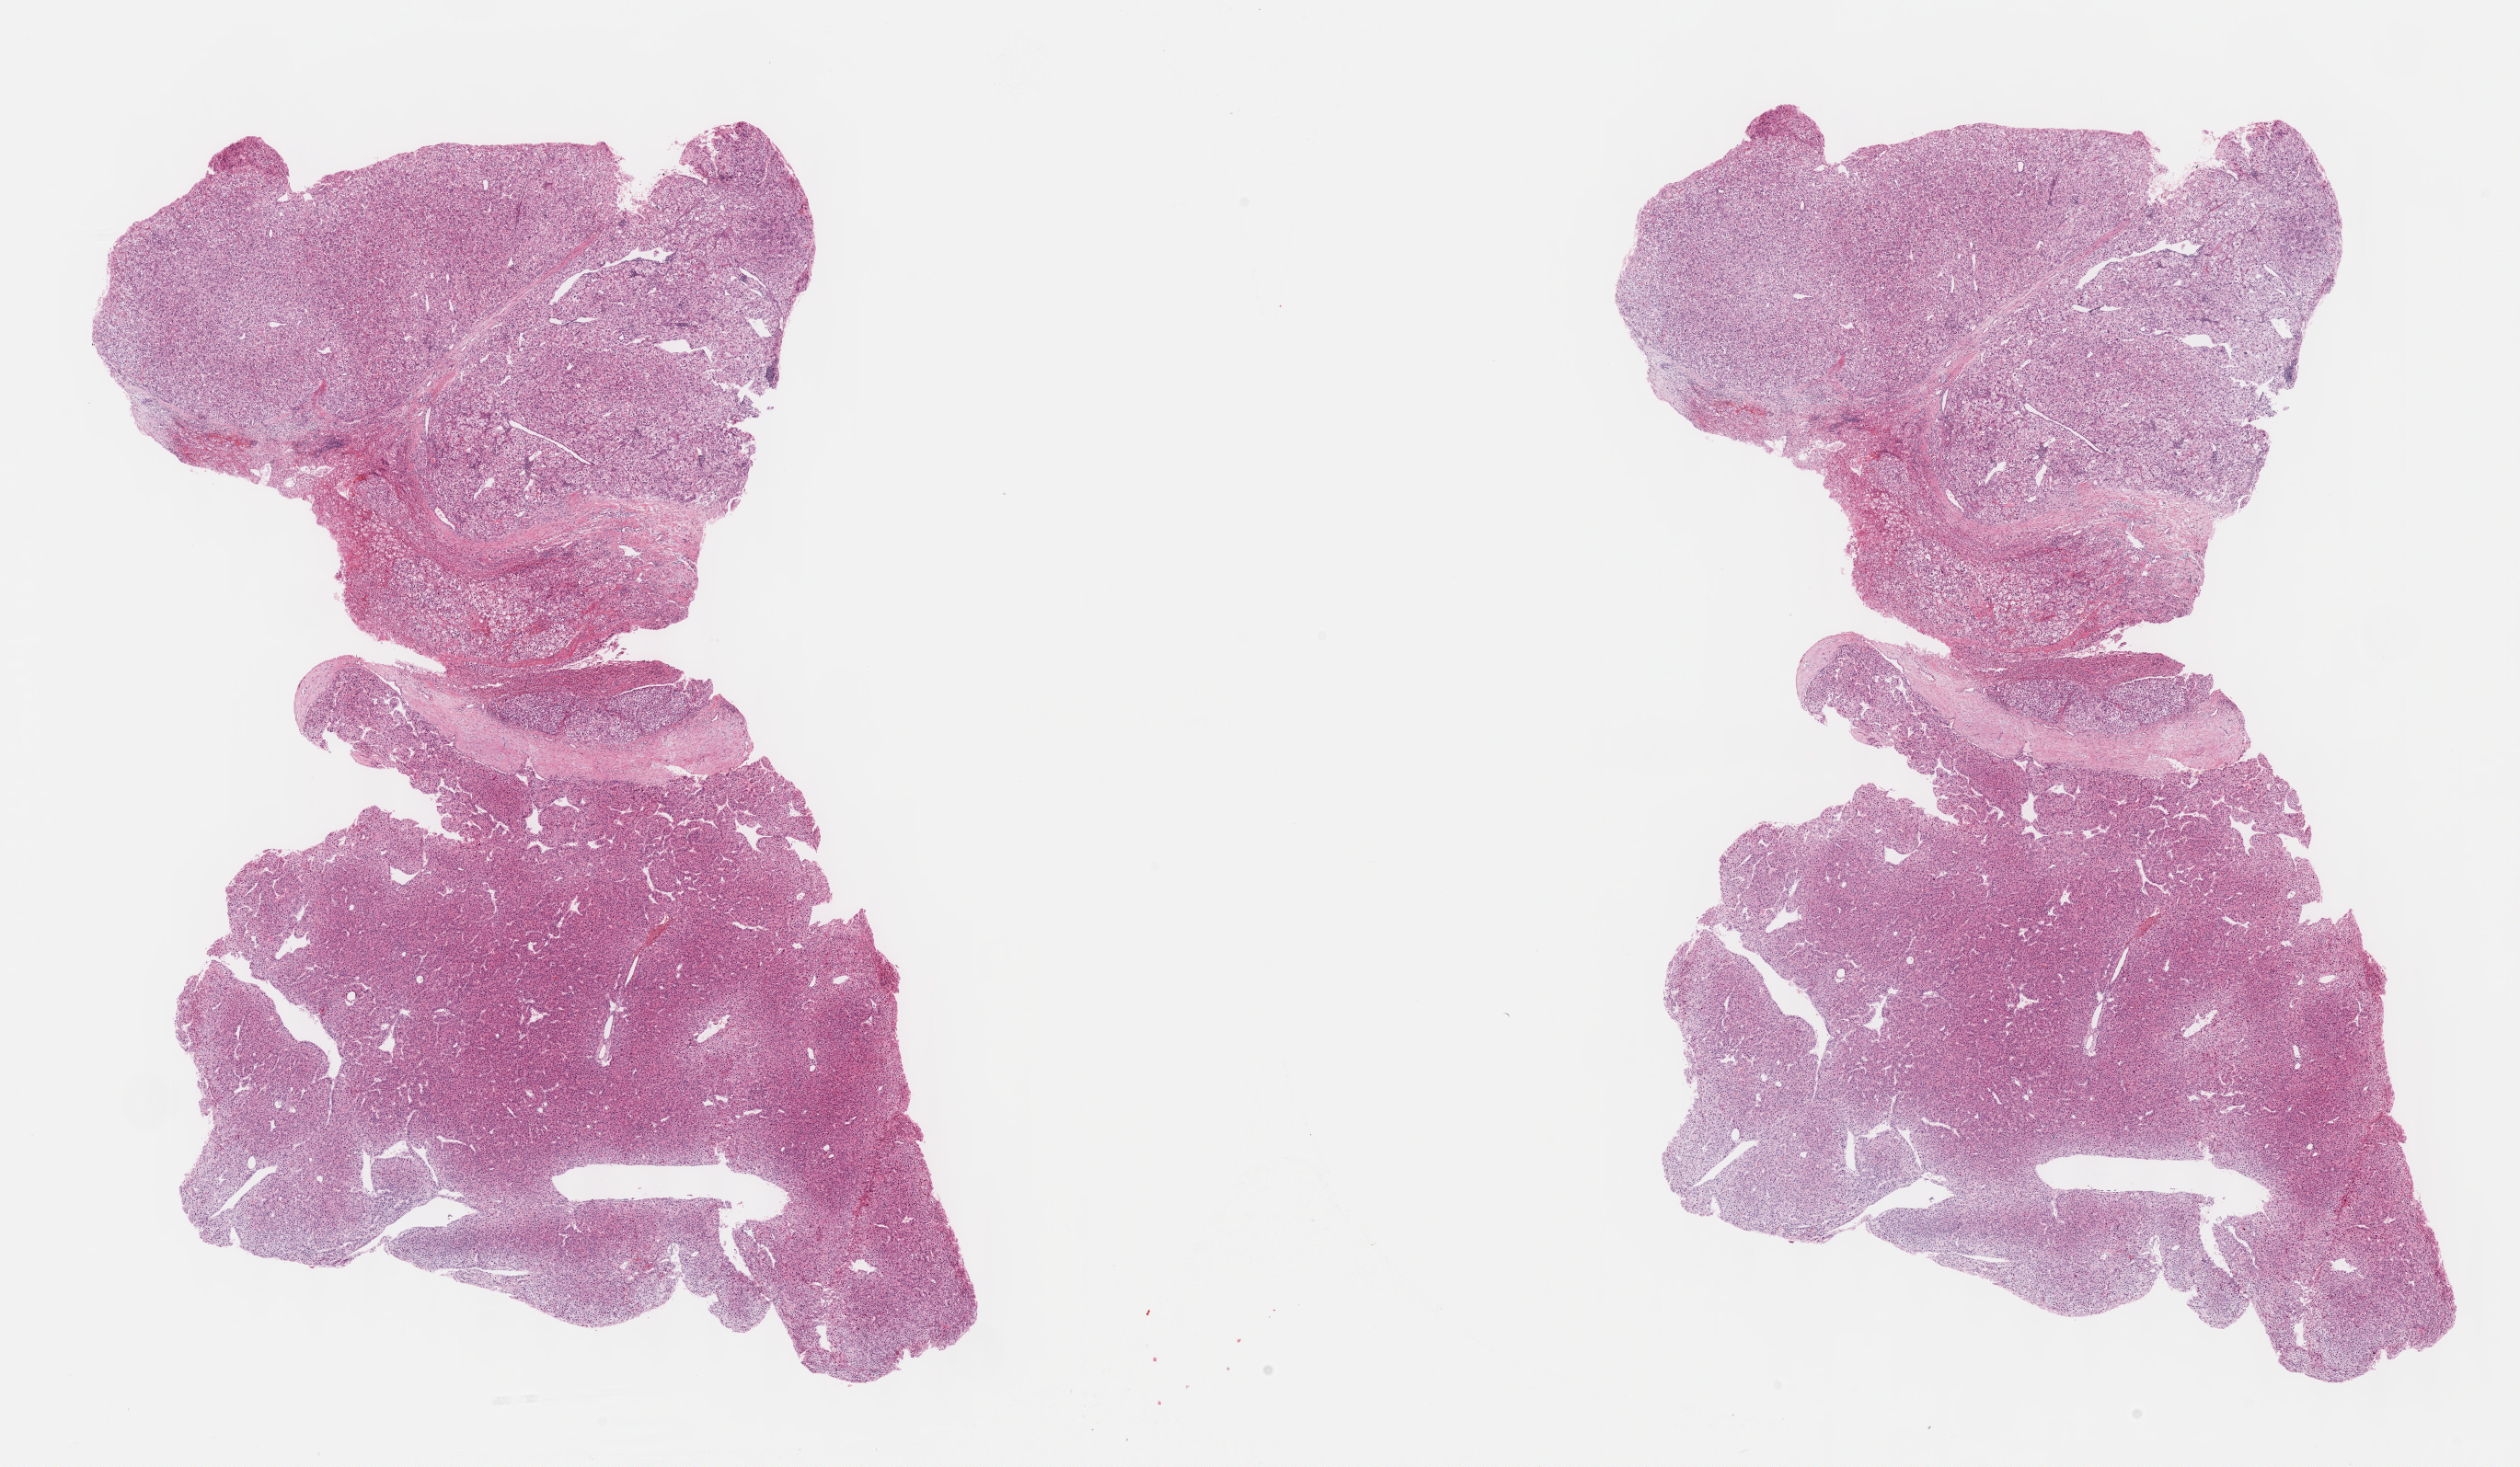
Digitized H&E-stained tissue section (whole slide) — whole scanned area (about 22.1 x 12.9 mm, acquisition: 40x scan) shown as a low-resolution overview; formalin-fixed paraffin-embedded (FFPE) diagnostic section; liver, primary tumour sample. Male, age 52 years at initial diagnosis. Histologic grade: G3 (poorly differentiated).
Diagnosis: Hepatocellular carcinoma, NOS. TNM: T1 N0 M0. AJCC pathologic stage: I (7th edition).